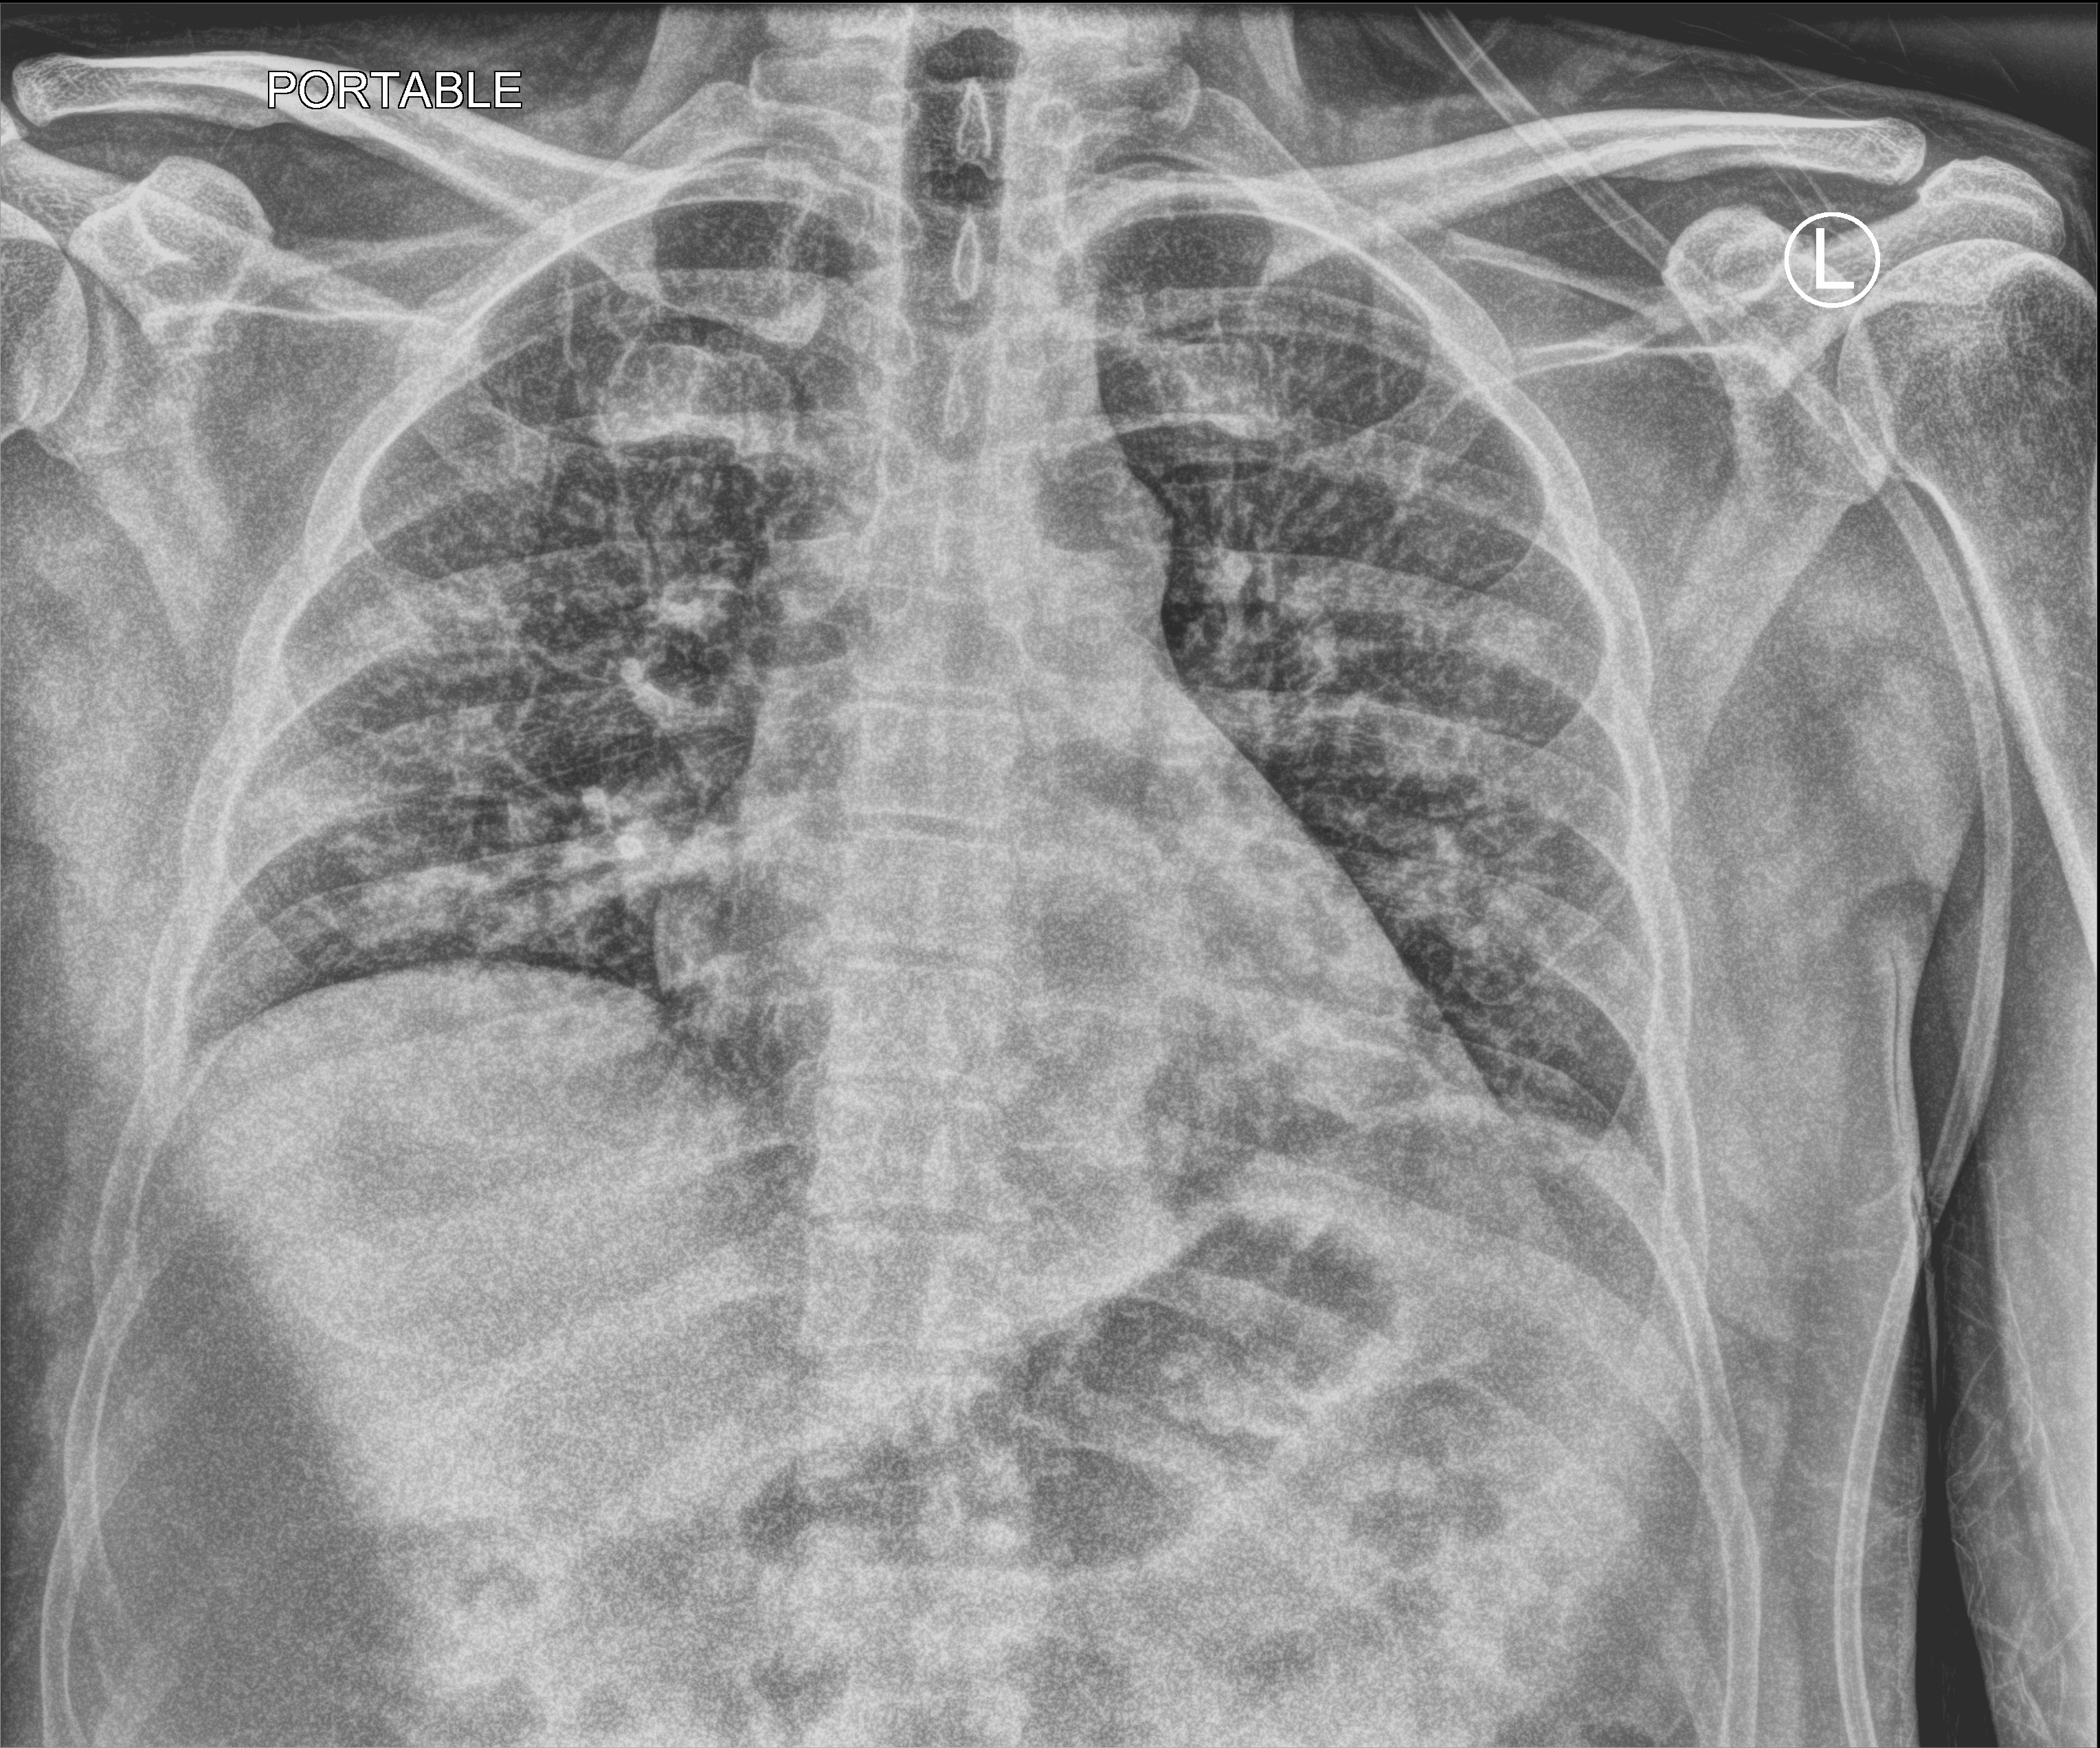
Portable chest radiograph; anteroposterior (AP) projection. Patient hospitalised with COVID-19; male, aged 18–59 years.
Admission-level facts for this patient (not findings on this image; timing relative to this image not recorded): mechanically ventilated during this hospital stay: no; admitted to intensive care during this hospital stay: no.